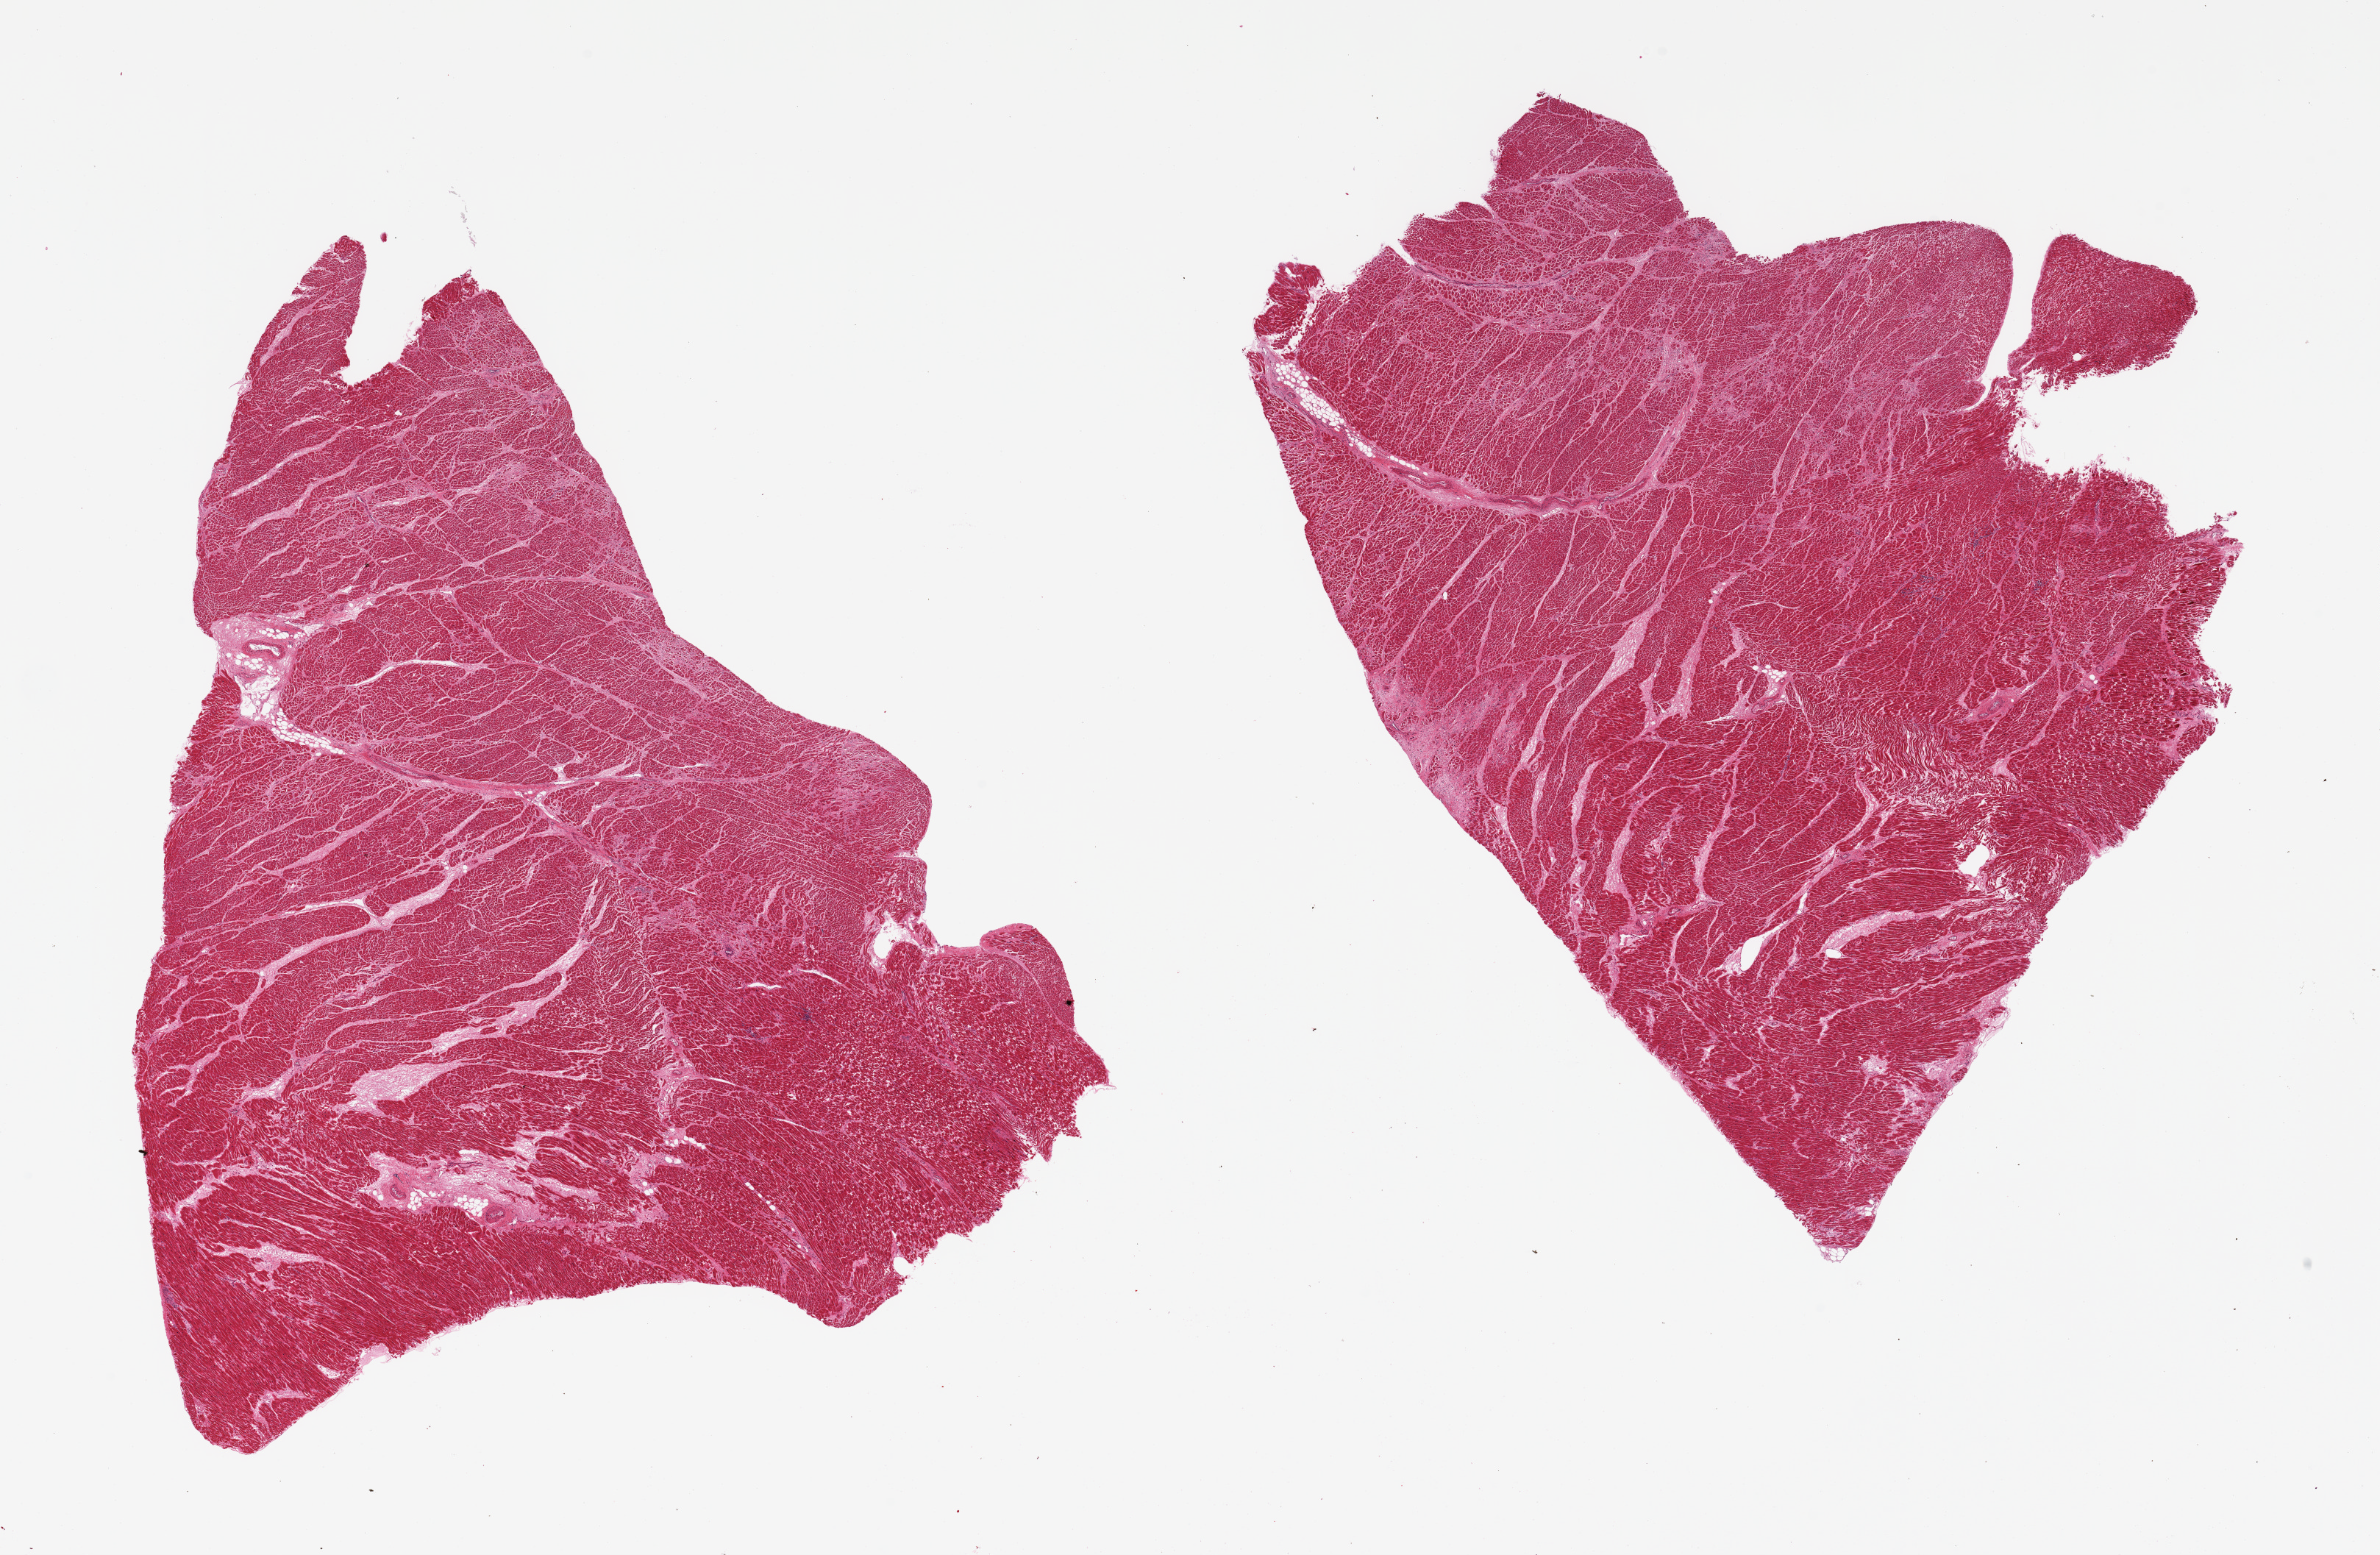
Whole-slide image, hematoxylin and eosin (H&E) stain, brightfield — a low-resolution overview of the entire scanned area, about 25.6 x 16.7 mm (from a 20x scan). PAXgene-fixed, paraffin-embedded tissue. Section of heart (target tissue). Tissue donor sample. Donor: male.
Reviewer comment on this tissue sample: 2 pieces, severe interstitial fibrosis/chronic ischemic damage with microinfarcts up to ~2mm.